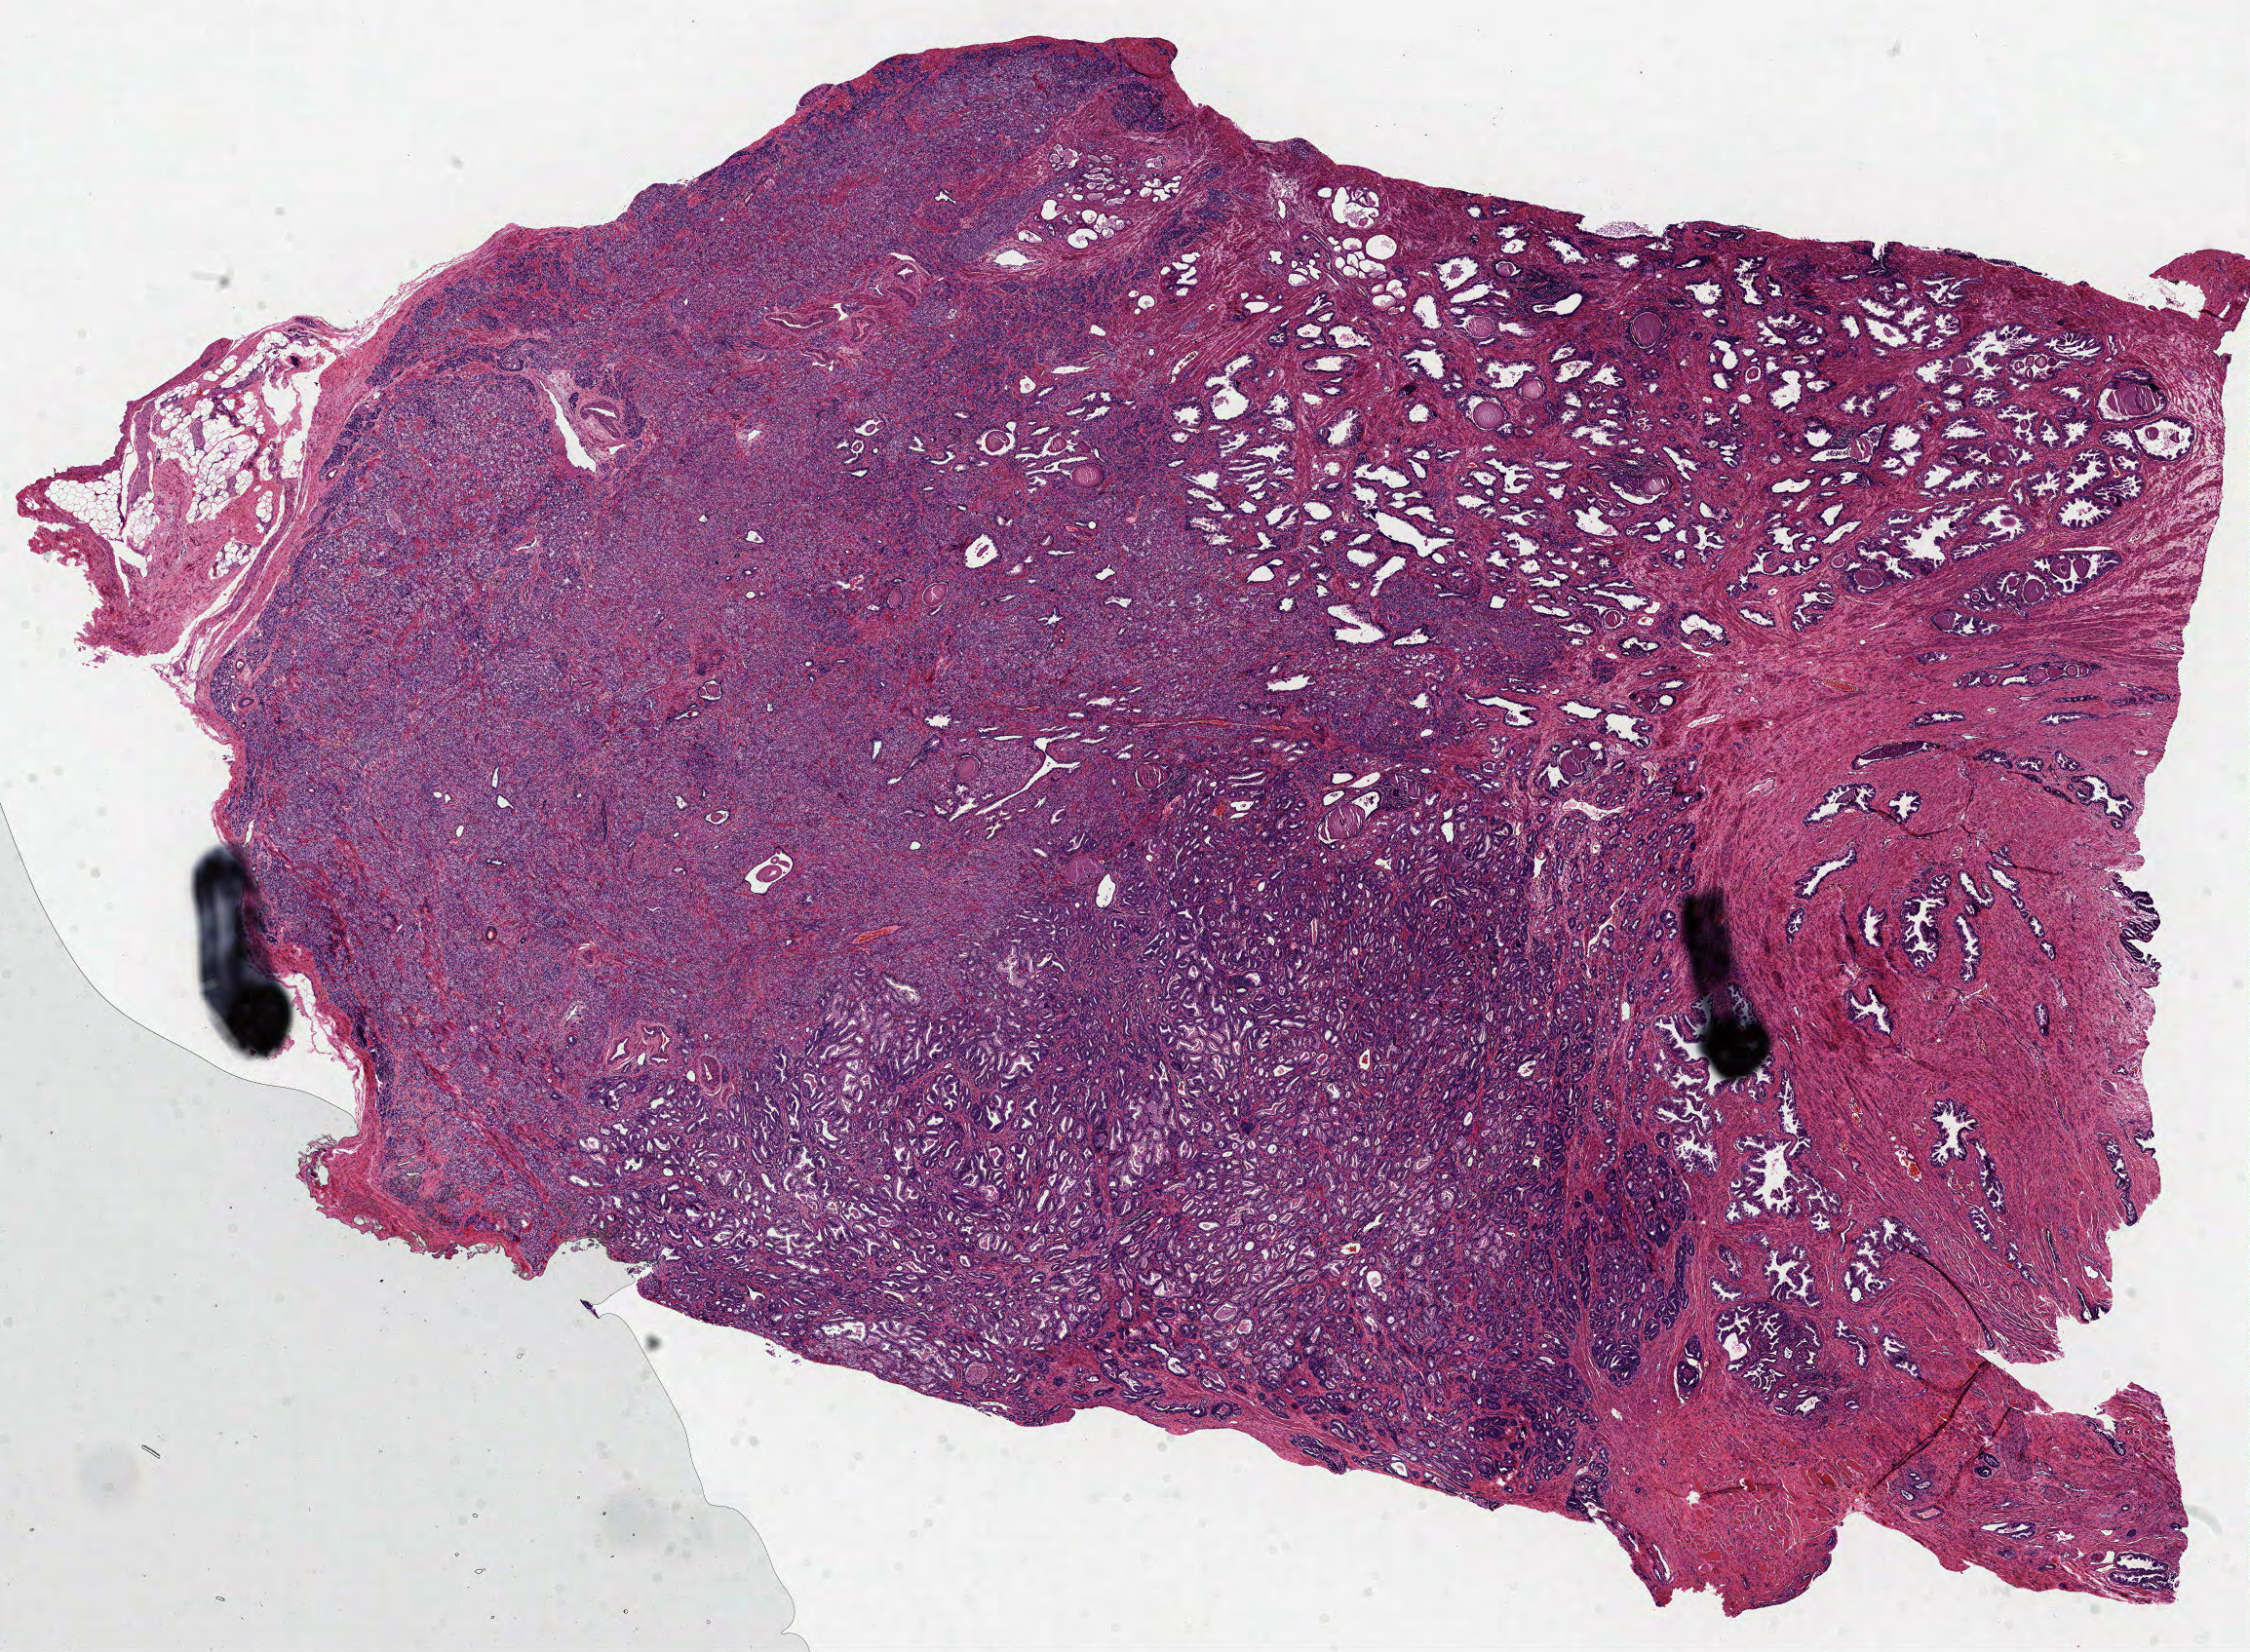
Whole-slide histology image, H&E, shown as a low-resolution overview of the whole scanned area (about 18.6 x 13.7 mm, slide scanned at 40x), formalin-fixed paraffin-embedded (FFPE) diagnostic section, sample: primary tumour, prostate. Male patient; age at initial diagnosis 50 years. Gleason score: 8 (5+3).
Pathologic diagnosis: Acinar cell carcinoma (prostate gland). Laterality: bilateral.